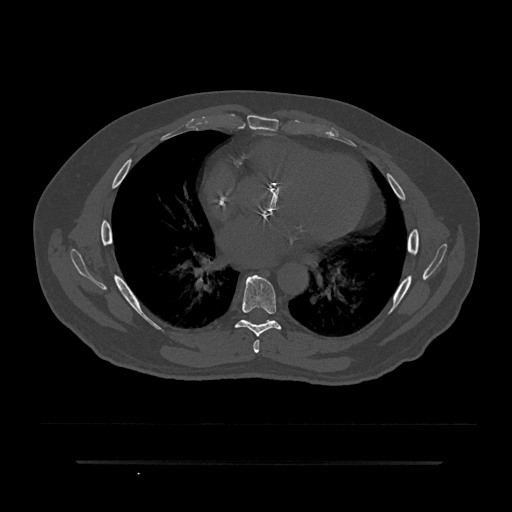
CT including the spine, one axial slice; slice 478 of 797 in the series (ordered by position); reconstruction kernel Br40s/3; bone window (W 1800 / L 400 HU); 0.5 mm slice thickness; 512 × 512 image matrix. Male patient, age 59 years. From the clinical record (not read from this slice): primary cancer: bile ducts; vertebrae with lytic lesions (as recorded): T10.
Outlined on this slice (semi-automatic segmentation, software-assisted and operator-edited):
- T6 vertebra: bounding box <253,340,260,353> (left, top, right, bottom; pixels)
- T7 vertebra: <235,275,282,337>